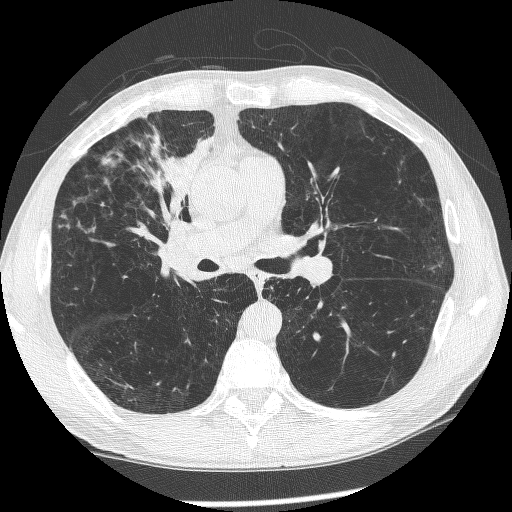
Chest CT (low-dose screening protocol), one axial image, first (baseline) screen, lung window (W 1500 / L -600 HU), 1.25 mm slice thickness, slice 139 of 266 in the series. Male, age 60 years at enrolment. Current smoker at enrolment.
Expert-annotated lung lesion, box from (x=145, y=182) to (x=217, y=276) px. Screening reader's record for this exam (one nodule recorded; not confirmed to be the boxed lesion): non-calcified nodule or mass ≥4 mm, right upper lobe, 12 × 8 mm, spiculated (stellate) margins, mixed attenuation. Official screen result: positive, change unspecified: nodule(s) >= 4 mm or enlarging nodule(s), mass(es), or other non-specific abnormalities suspicious for lung cancer. Lung cancer was diagnosed 208 days after this screen: squamous cell carcinoma, NOS, right upper lobe, right middle lobe, right main stem bronchus, poorly differentiated (G3), stage IV (AJCC 6th edition).